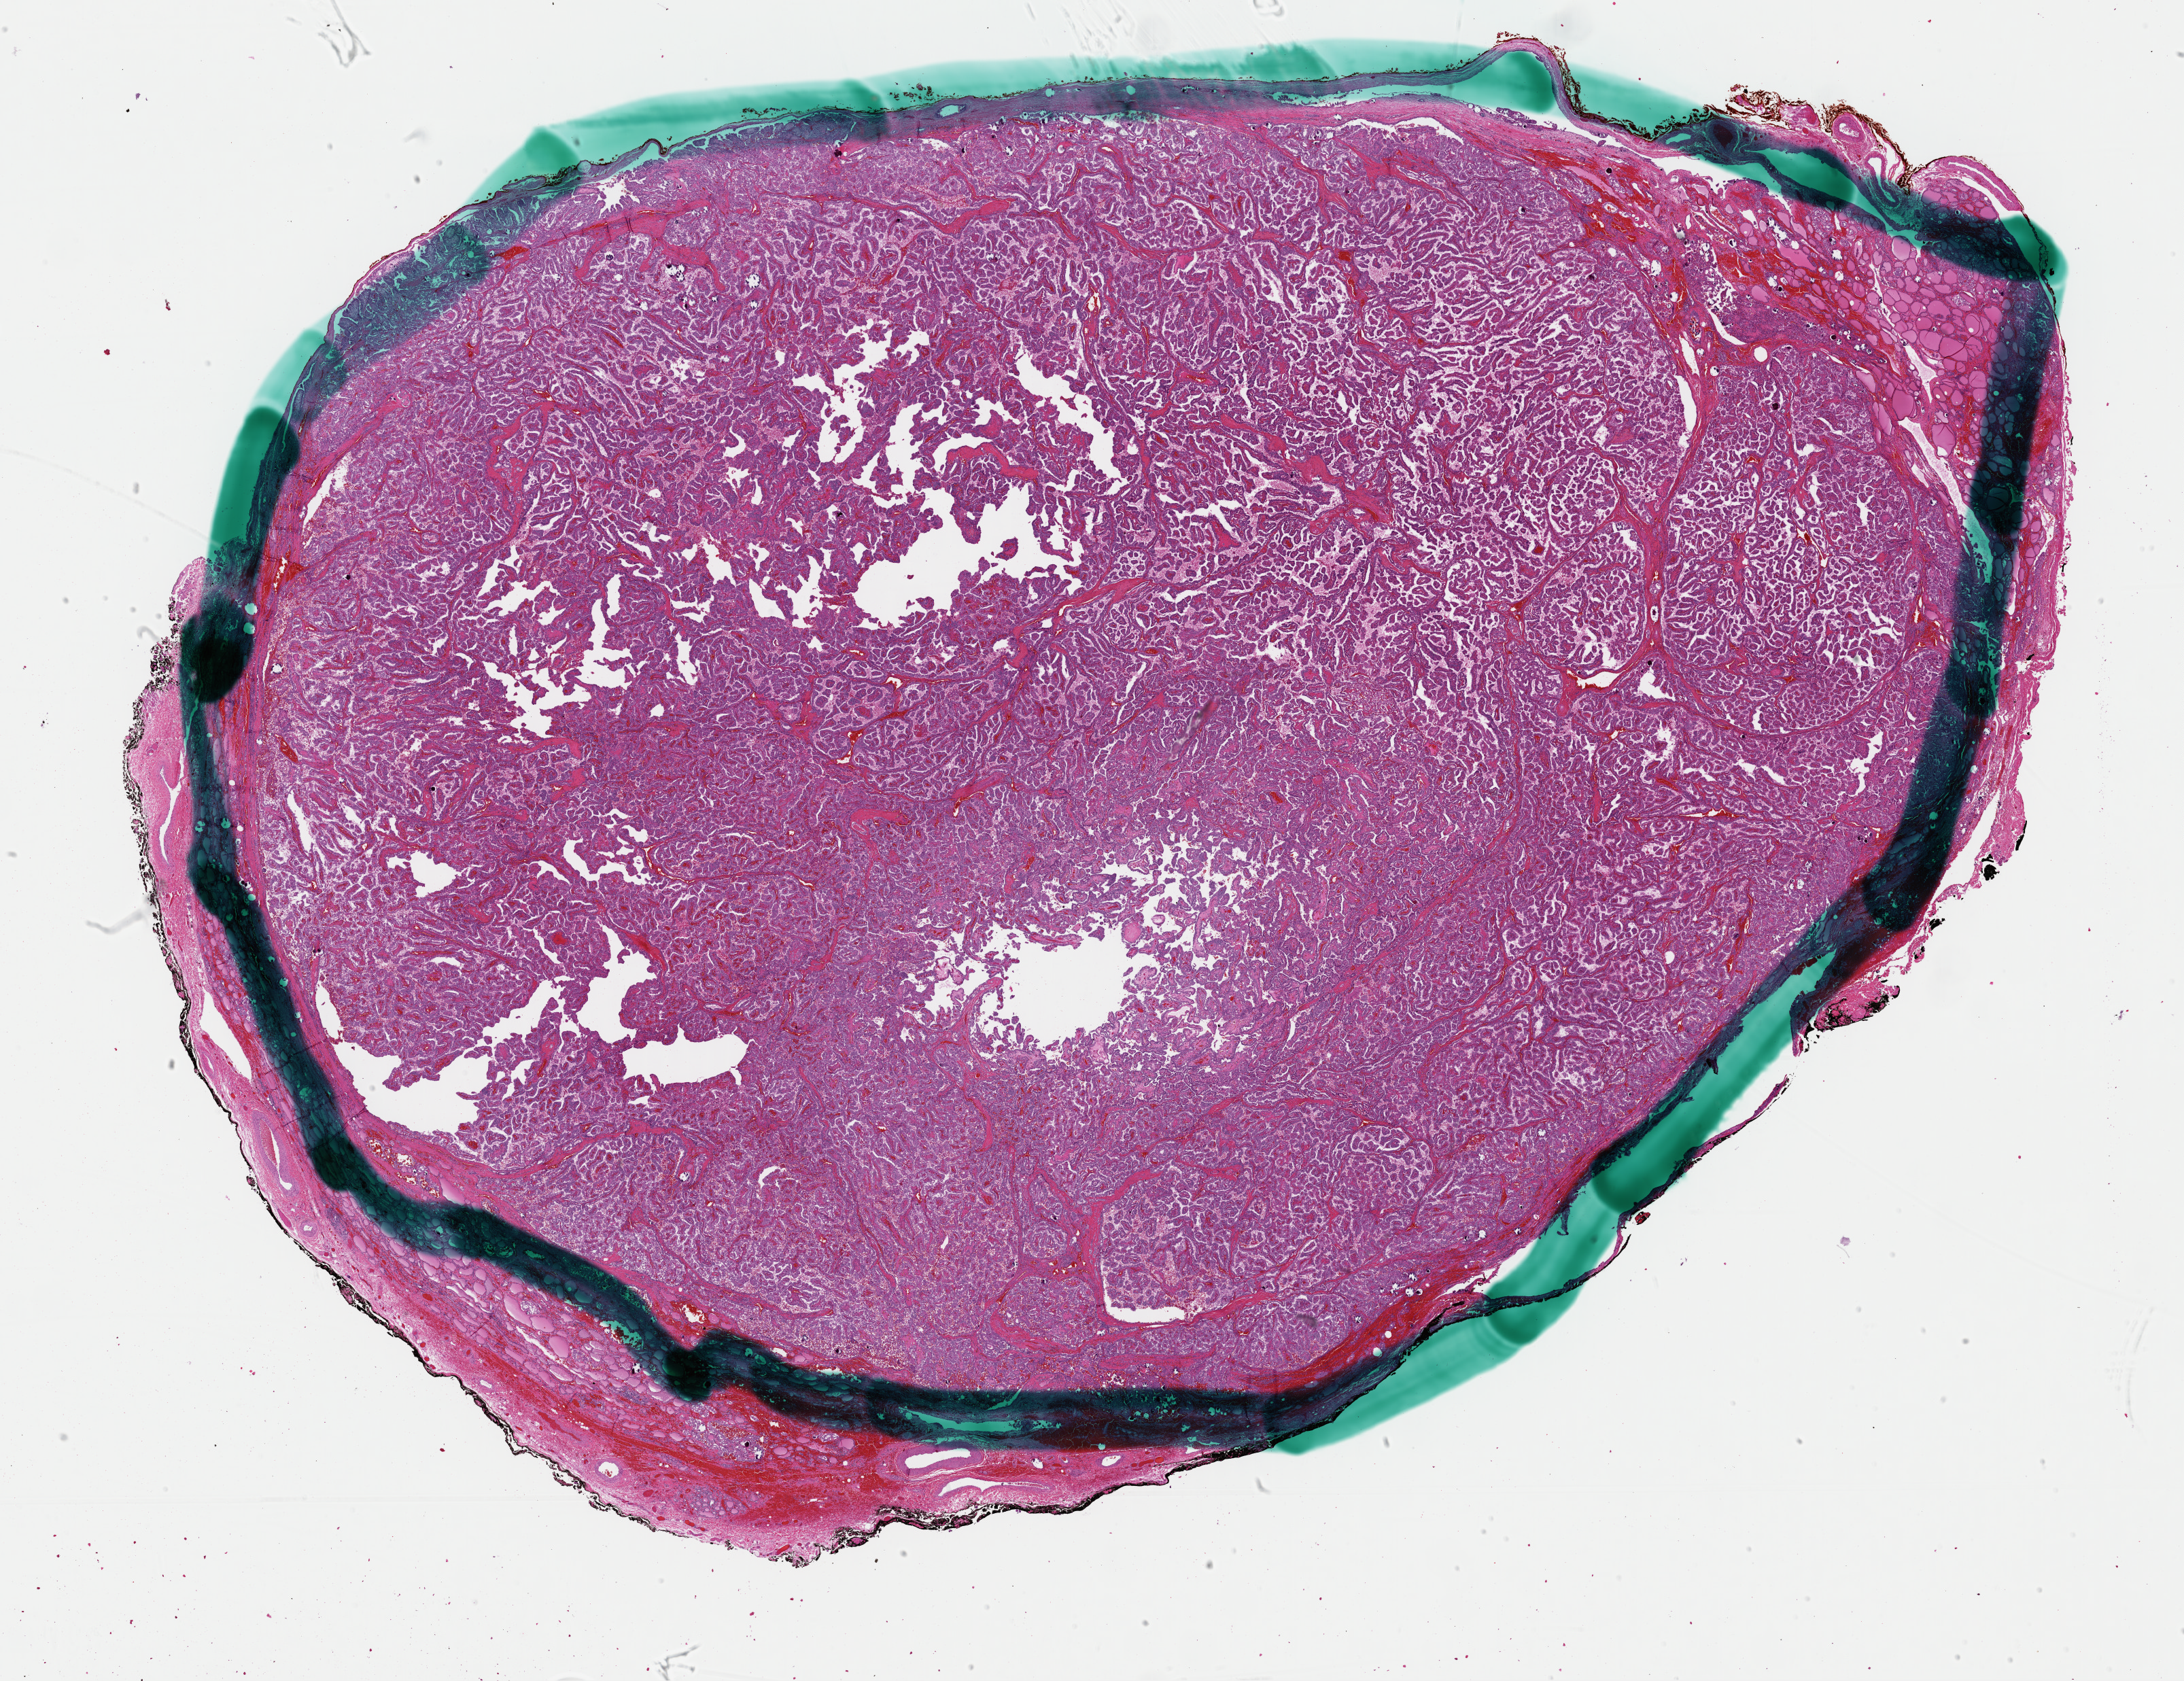
Hematoxylin and eosin (H&E) stained whole-slide image, shown as a low-resolution overview of the whole scanned area (about 25.4 x 19.5 mm), formalin-fixed paraffin-embedded (FFPE) diagnostic section, thyroid, primary tumour sample. Female patient; age at initial diagnosis 21 years.
Histologic diagnosis: Papillary adenocarcinoma, NOS (thyroid gland).